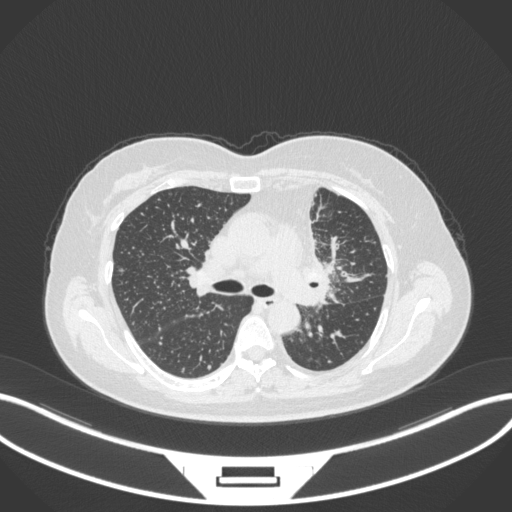
Chest CT, one axial slice; slice 209 of 348 in the series (ordered by position); reconstruction kernel B31f; 120 kVp; lung window (W 1500 / L -600 HU); 512 × 512 image matrix, field of view 400 × 400 mm. Female patient, age 49 years. Case-level facts recorded for this patient, not image findings: clinical TNM (as recorded): T1c N0 M1.
Annotated regions visible in this slice (bounding box drawn by a radiologist):
- lung tumour (recorded histology: adenocarcinoma): box from (x=298, y=250) to (x=337, y=313) px